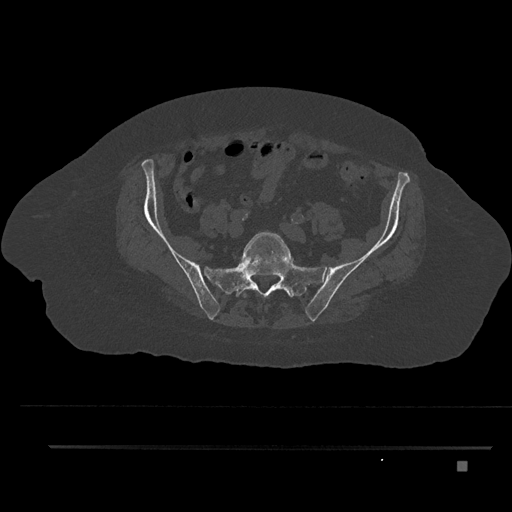
CT including the spine, one axial slice; 120 kVp; bone window (W 1800 / L 400 HU); 0.5 mm slice thickness; 512 × 512 image matrix, field of view 437 × 437 mm. Patient: female, 76 years. From the clinical record (not read from this slice): primary cancer: lung; vertebrae with lytic lesions (as recorded): T11, L3.
Annotated regions visible in this slice (semi-automatically segmented with operator editing):
- L5 vertebra: bounding box [x1, y1, x2, y2] px = [242, 231, 290, 298]